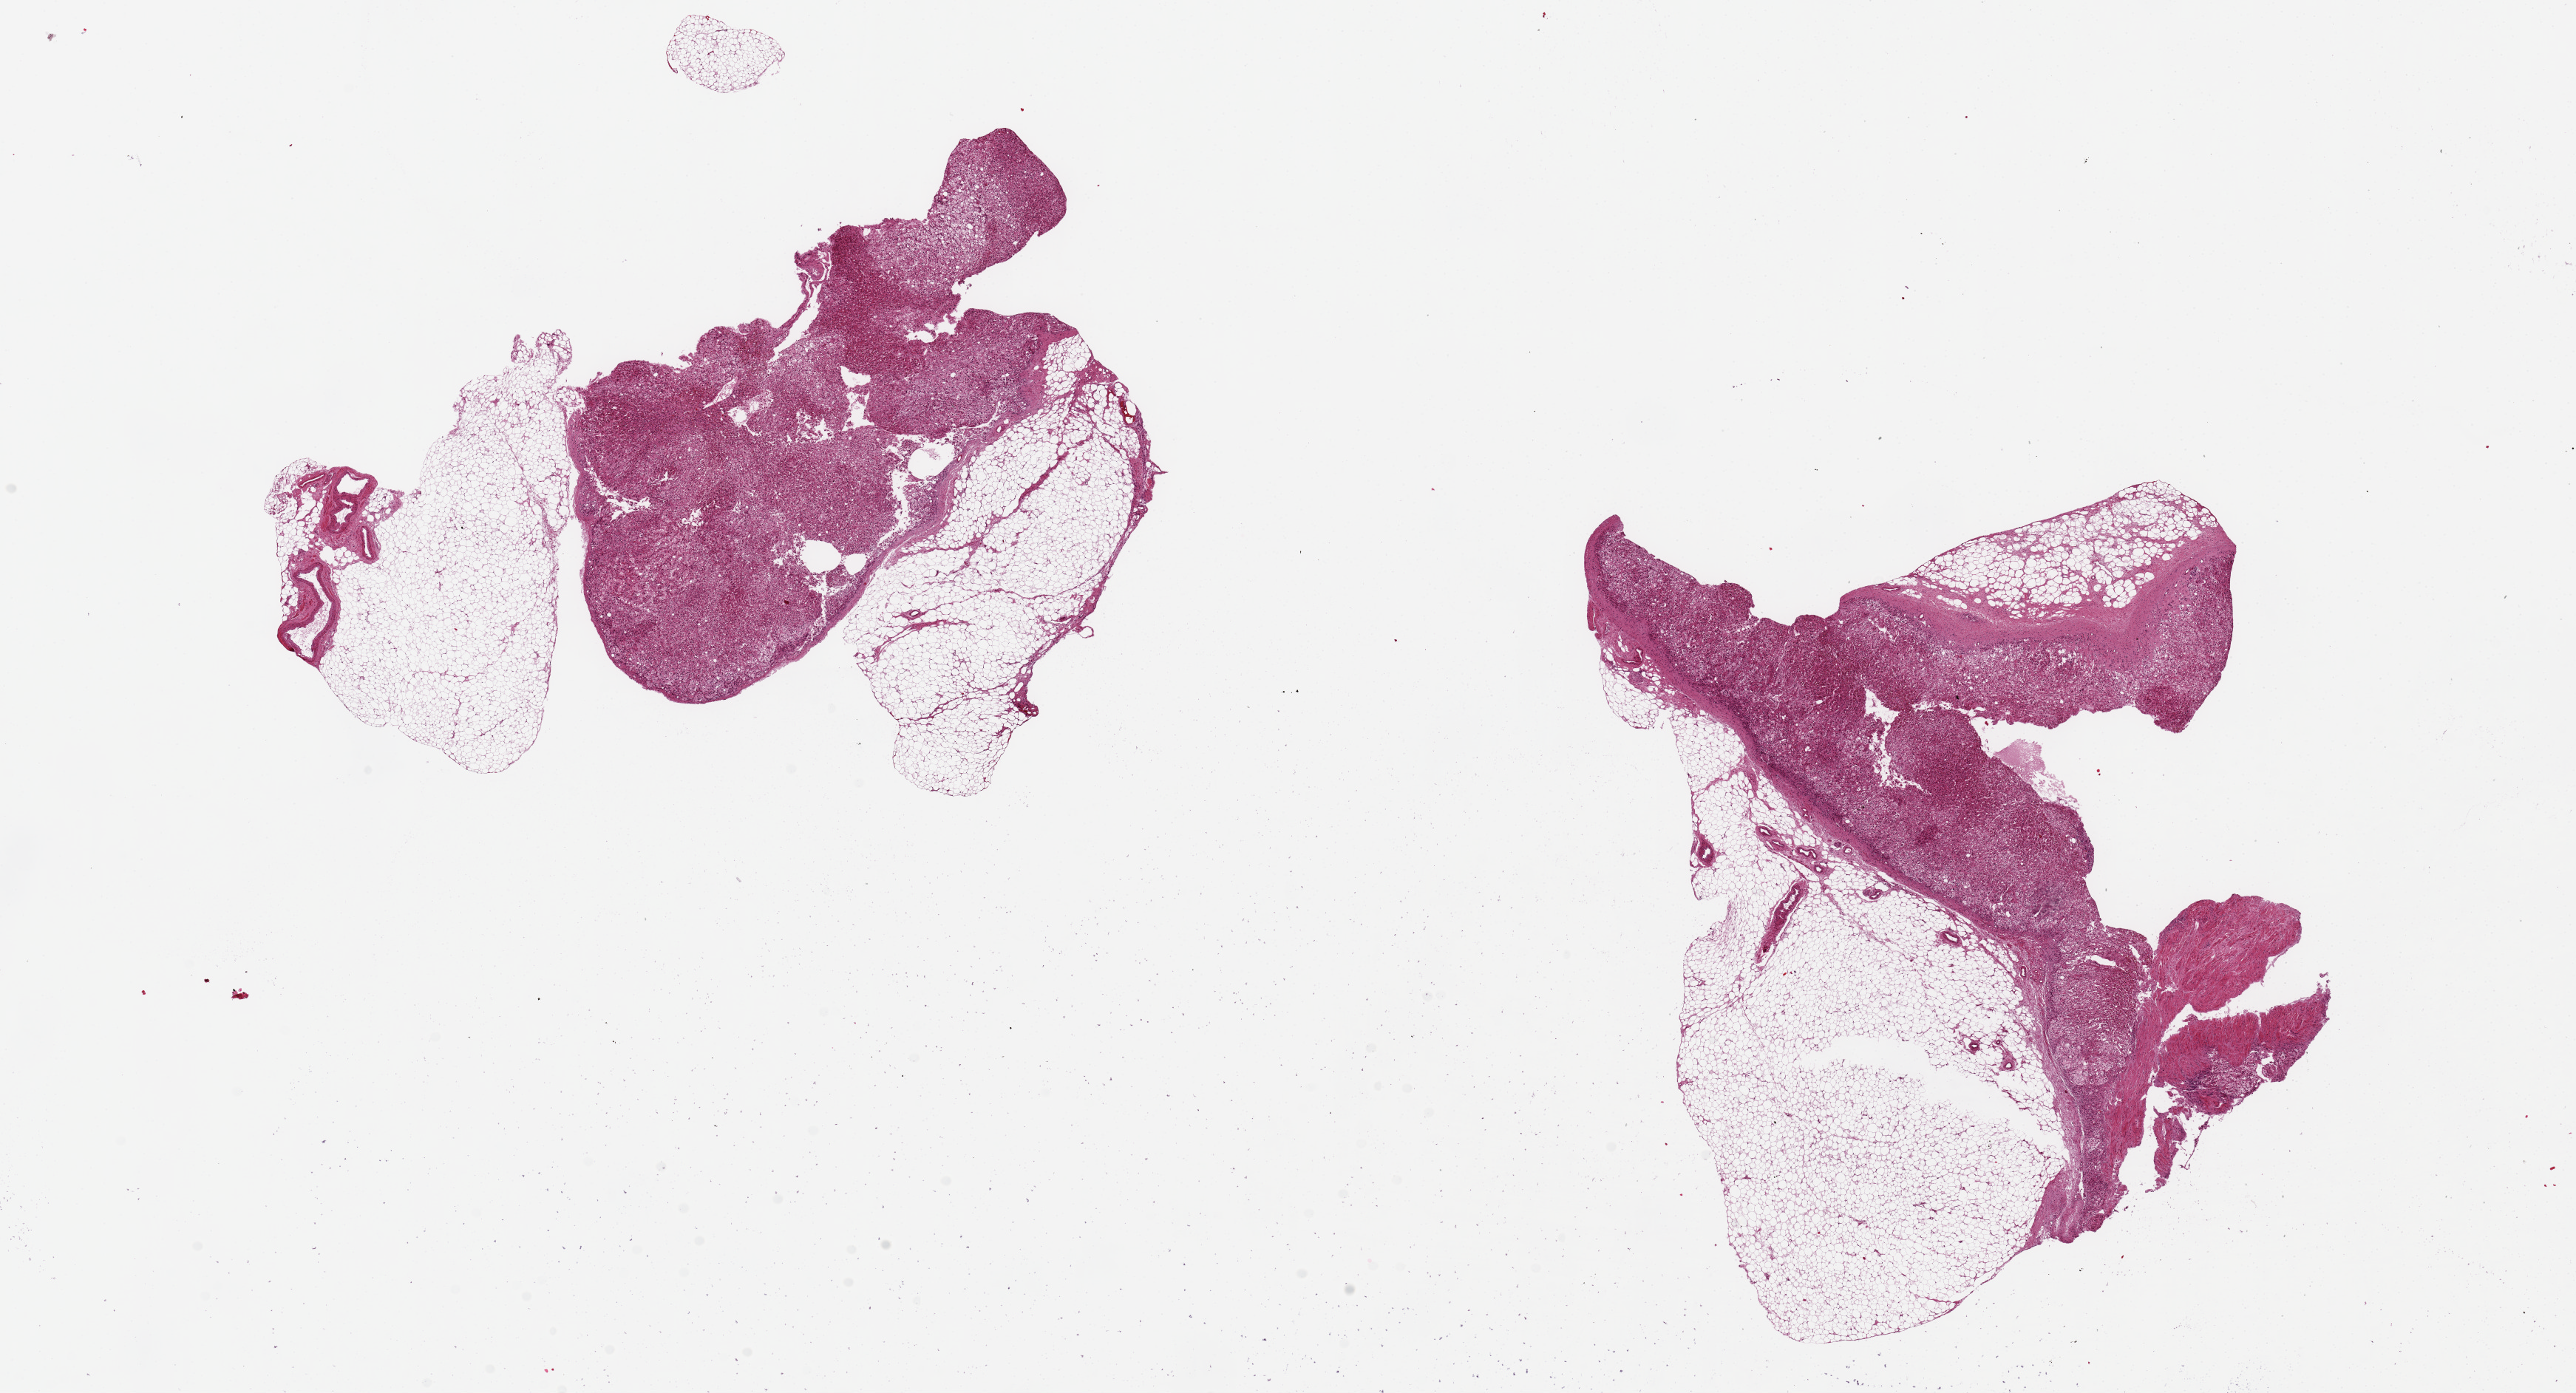
H&E whole-slide image, brightfield, low-resolution overview of the scanned area, about 27.6 x 14.9 mm, PAXgene-fixed, paraffin-embedded tissue, target tissue: adrenal gland, donor tissue sample.
Pathologist's review note for this sample: 2pieces ~7x4mm, adherent nubbins of fat up to ~4-3mm in dimensions on both.